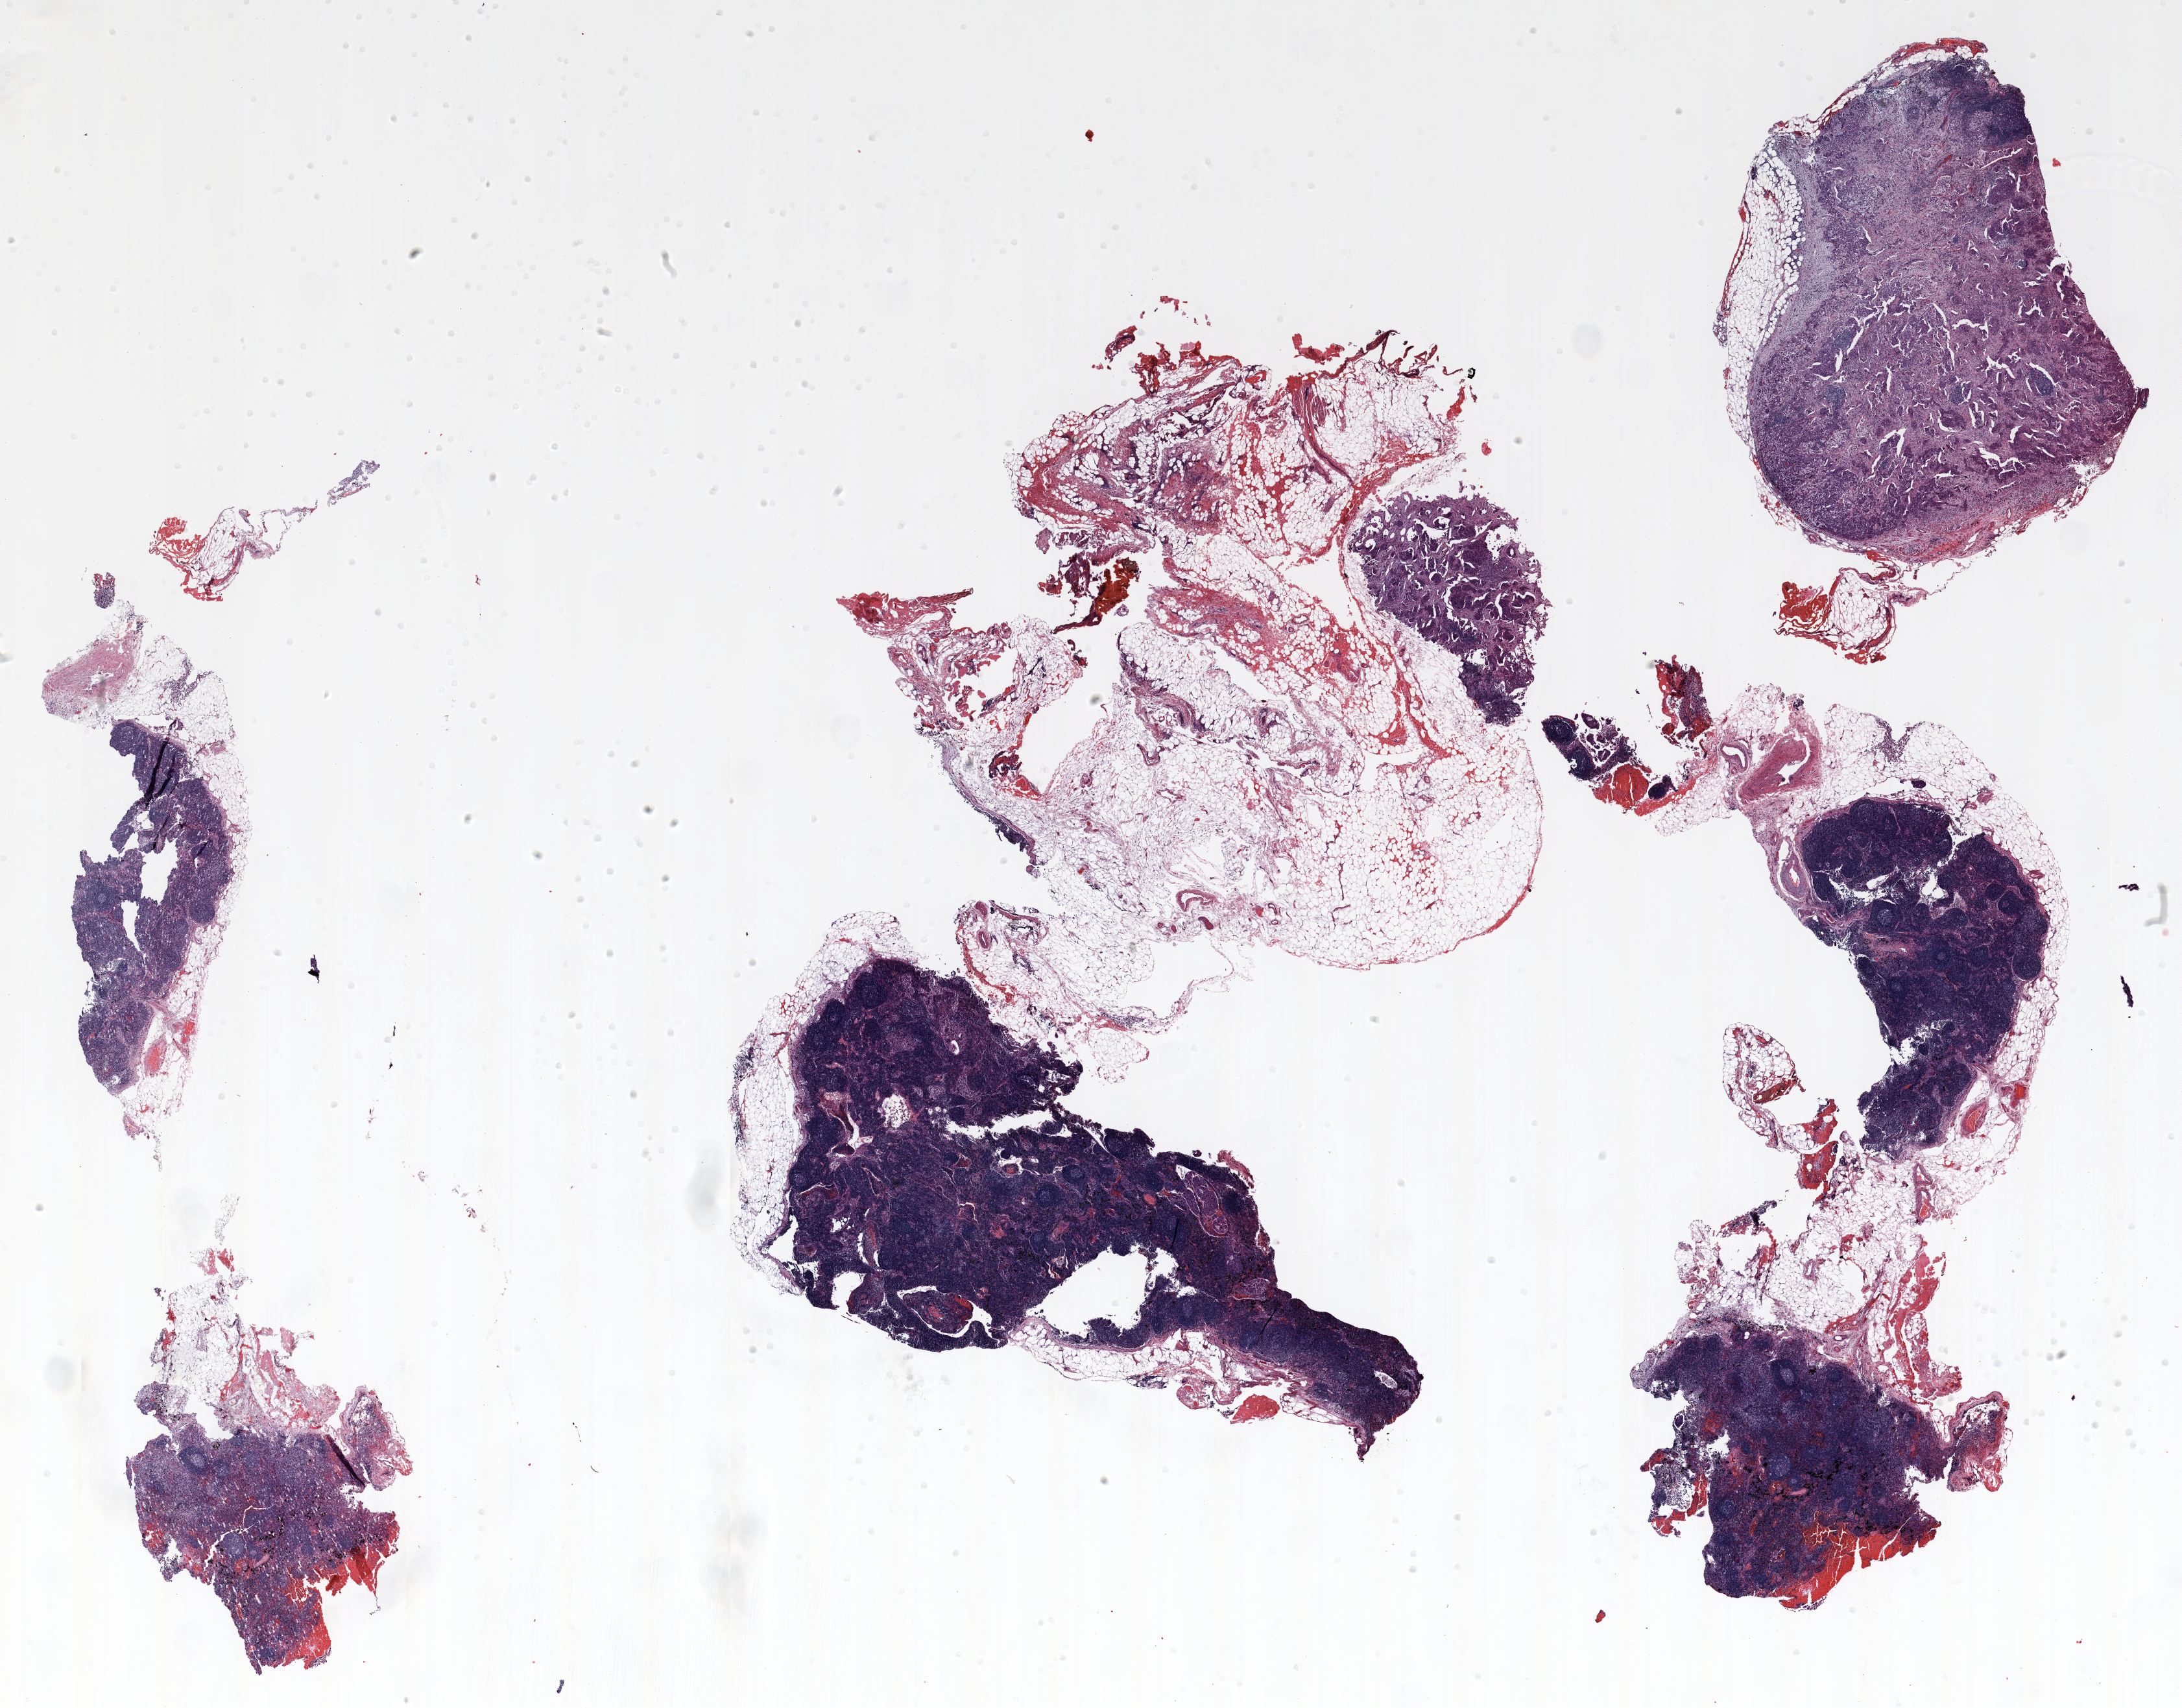
Whole-slide histology image, H&E — low-resolution overview of the scanned area, about 27.0 x 21.2 mm (acquisition: 20x scan); formalin-fixed paraffin-embedded (FFPE) section; lung tissue. Male patient, aged 59 at enrolment. Former smoker at enrolment. Grade: poorly differentiated (G3).
* participant's lung-cancer diagnosis: Signet ring cell carcinoma (ICD-O-3 8490/3)
* primary tumour location (clinical record): left lower lobe
* stage (AJCC 6th edition): IIIA
* tumour size (pathology): 21 mm